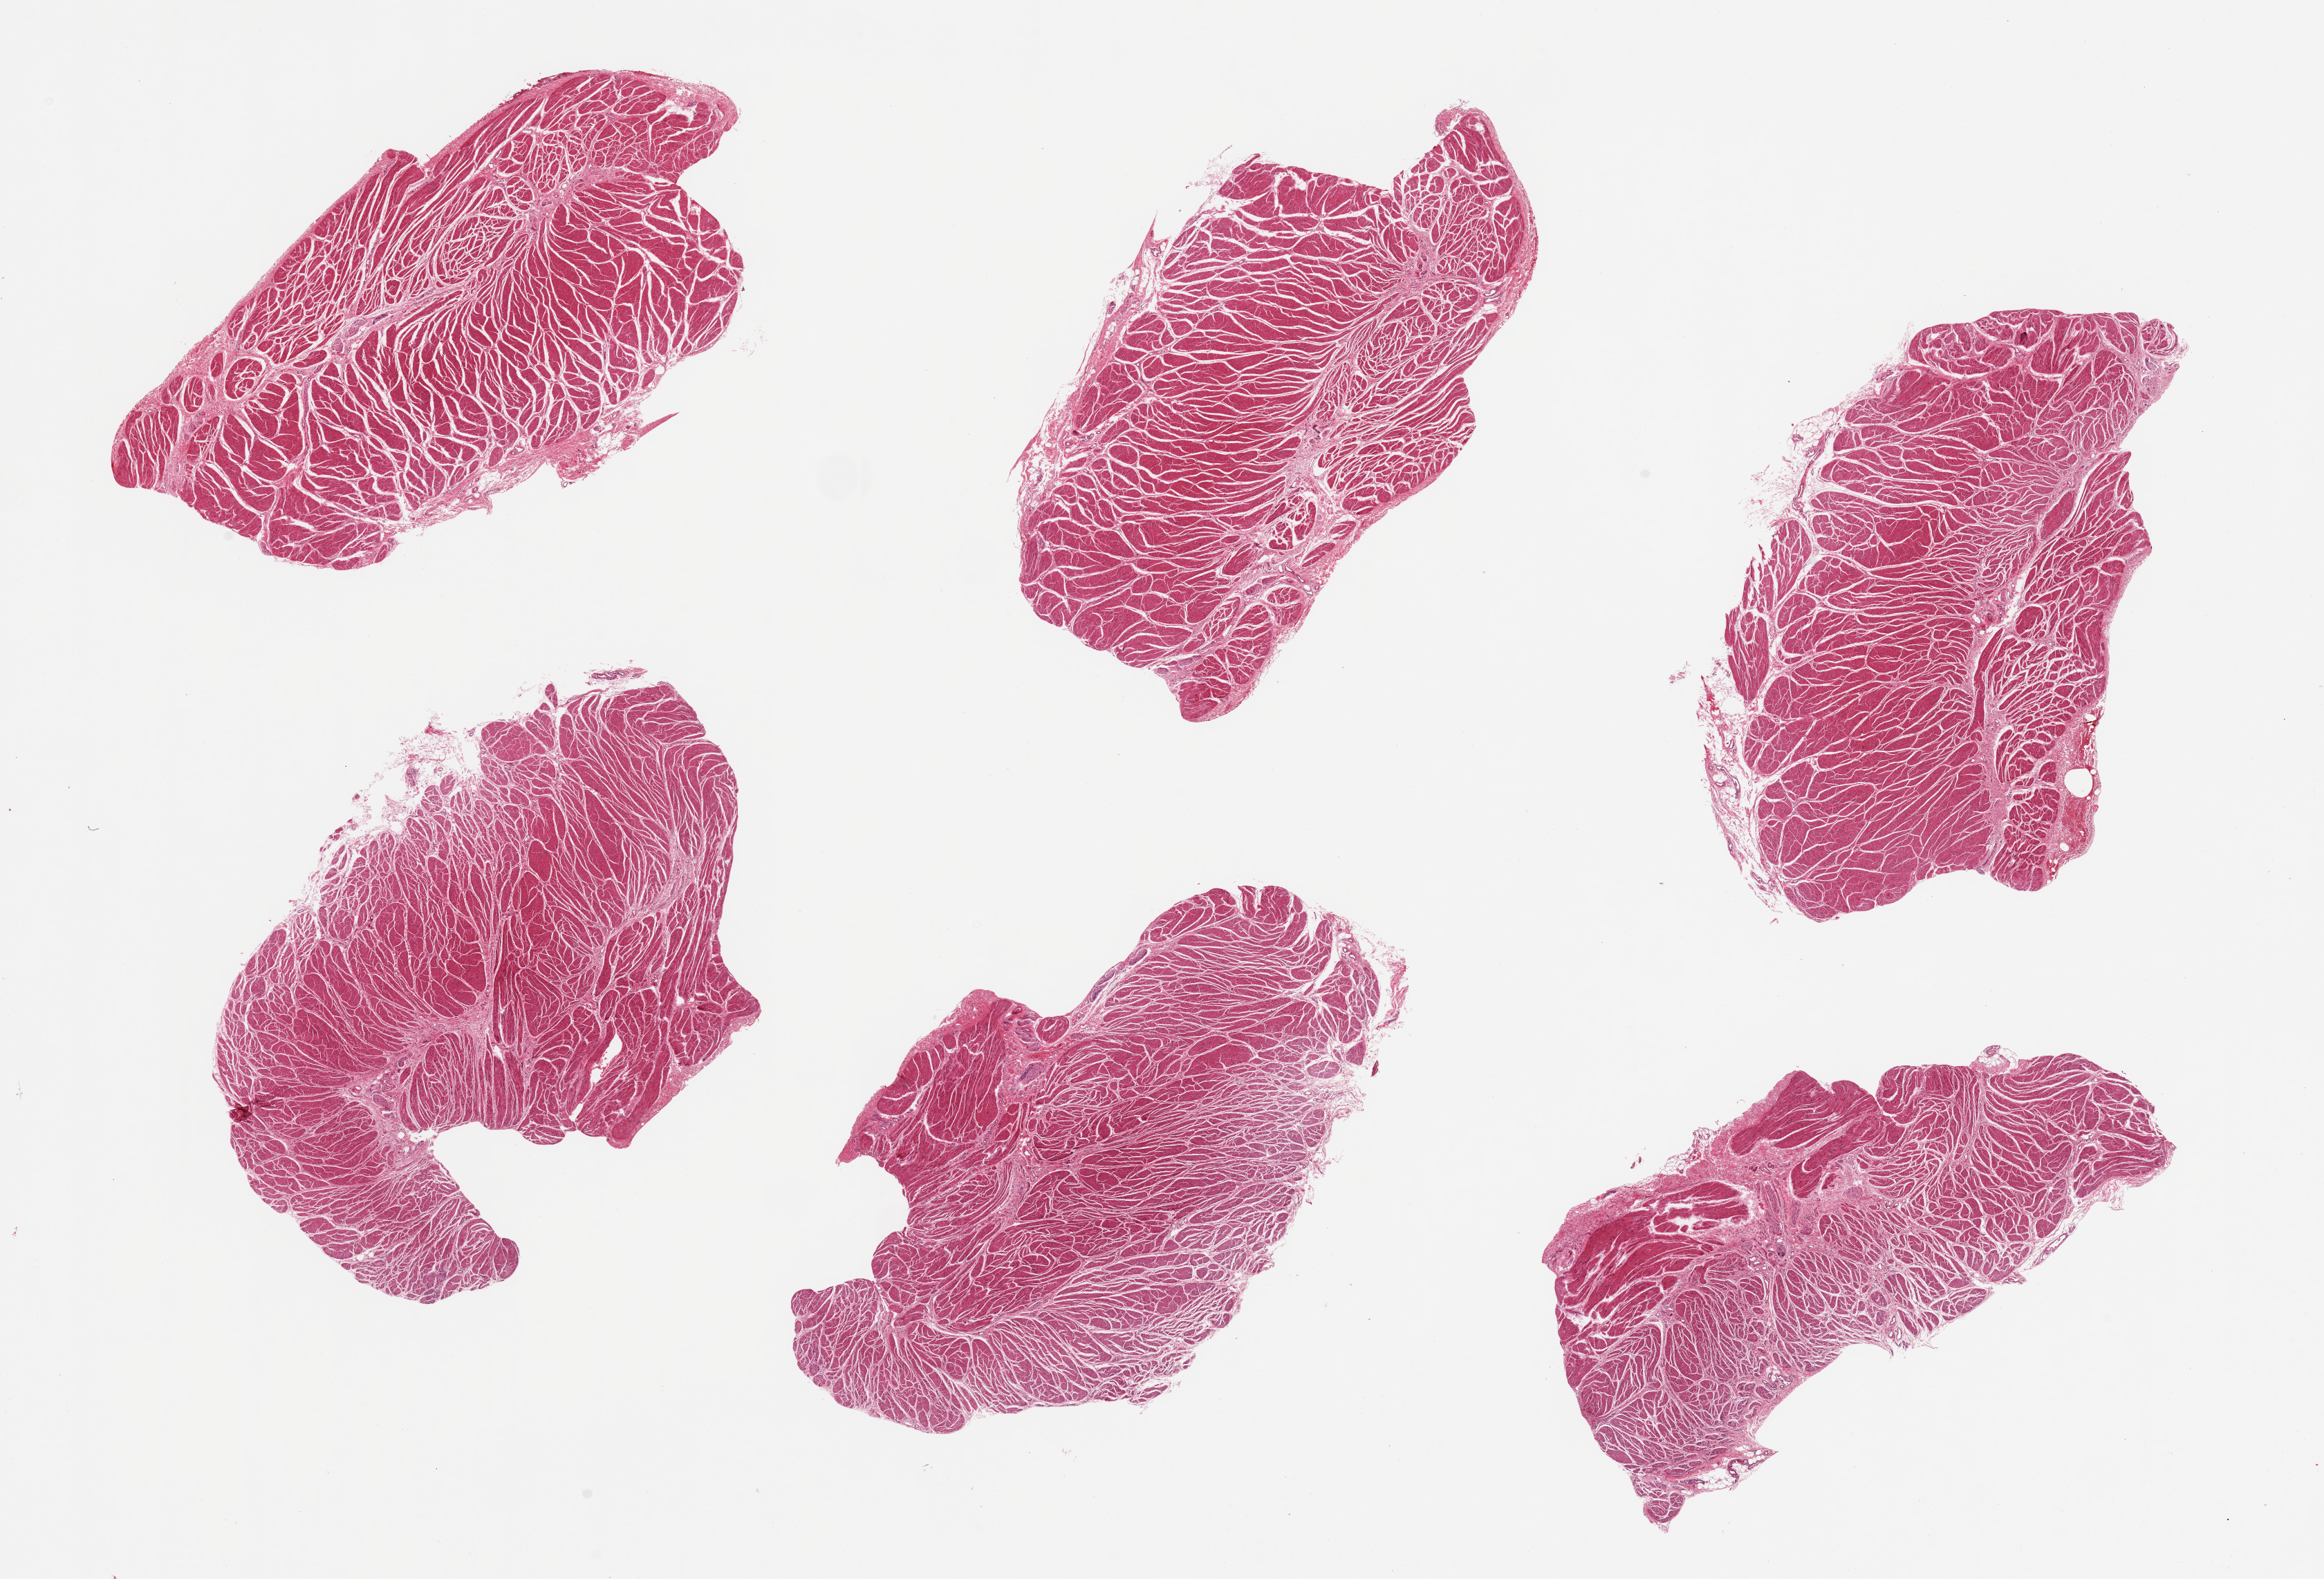
Digitized H&E-stained section, low-resolution overview of the scanned area, about 26.6 x 18.1 mm (slide scanned at 20x). PAXgene-fixed paraffin-embedded (PFPE) section. Sampled site (target tissue): gastroesophageal junction. Tissue donor sample. Donor sex: male.
Reviewer comment on this tissue sample: 6 pieces. well trimmed muscularis.